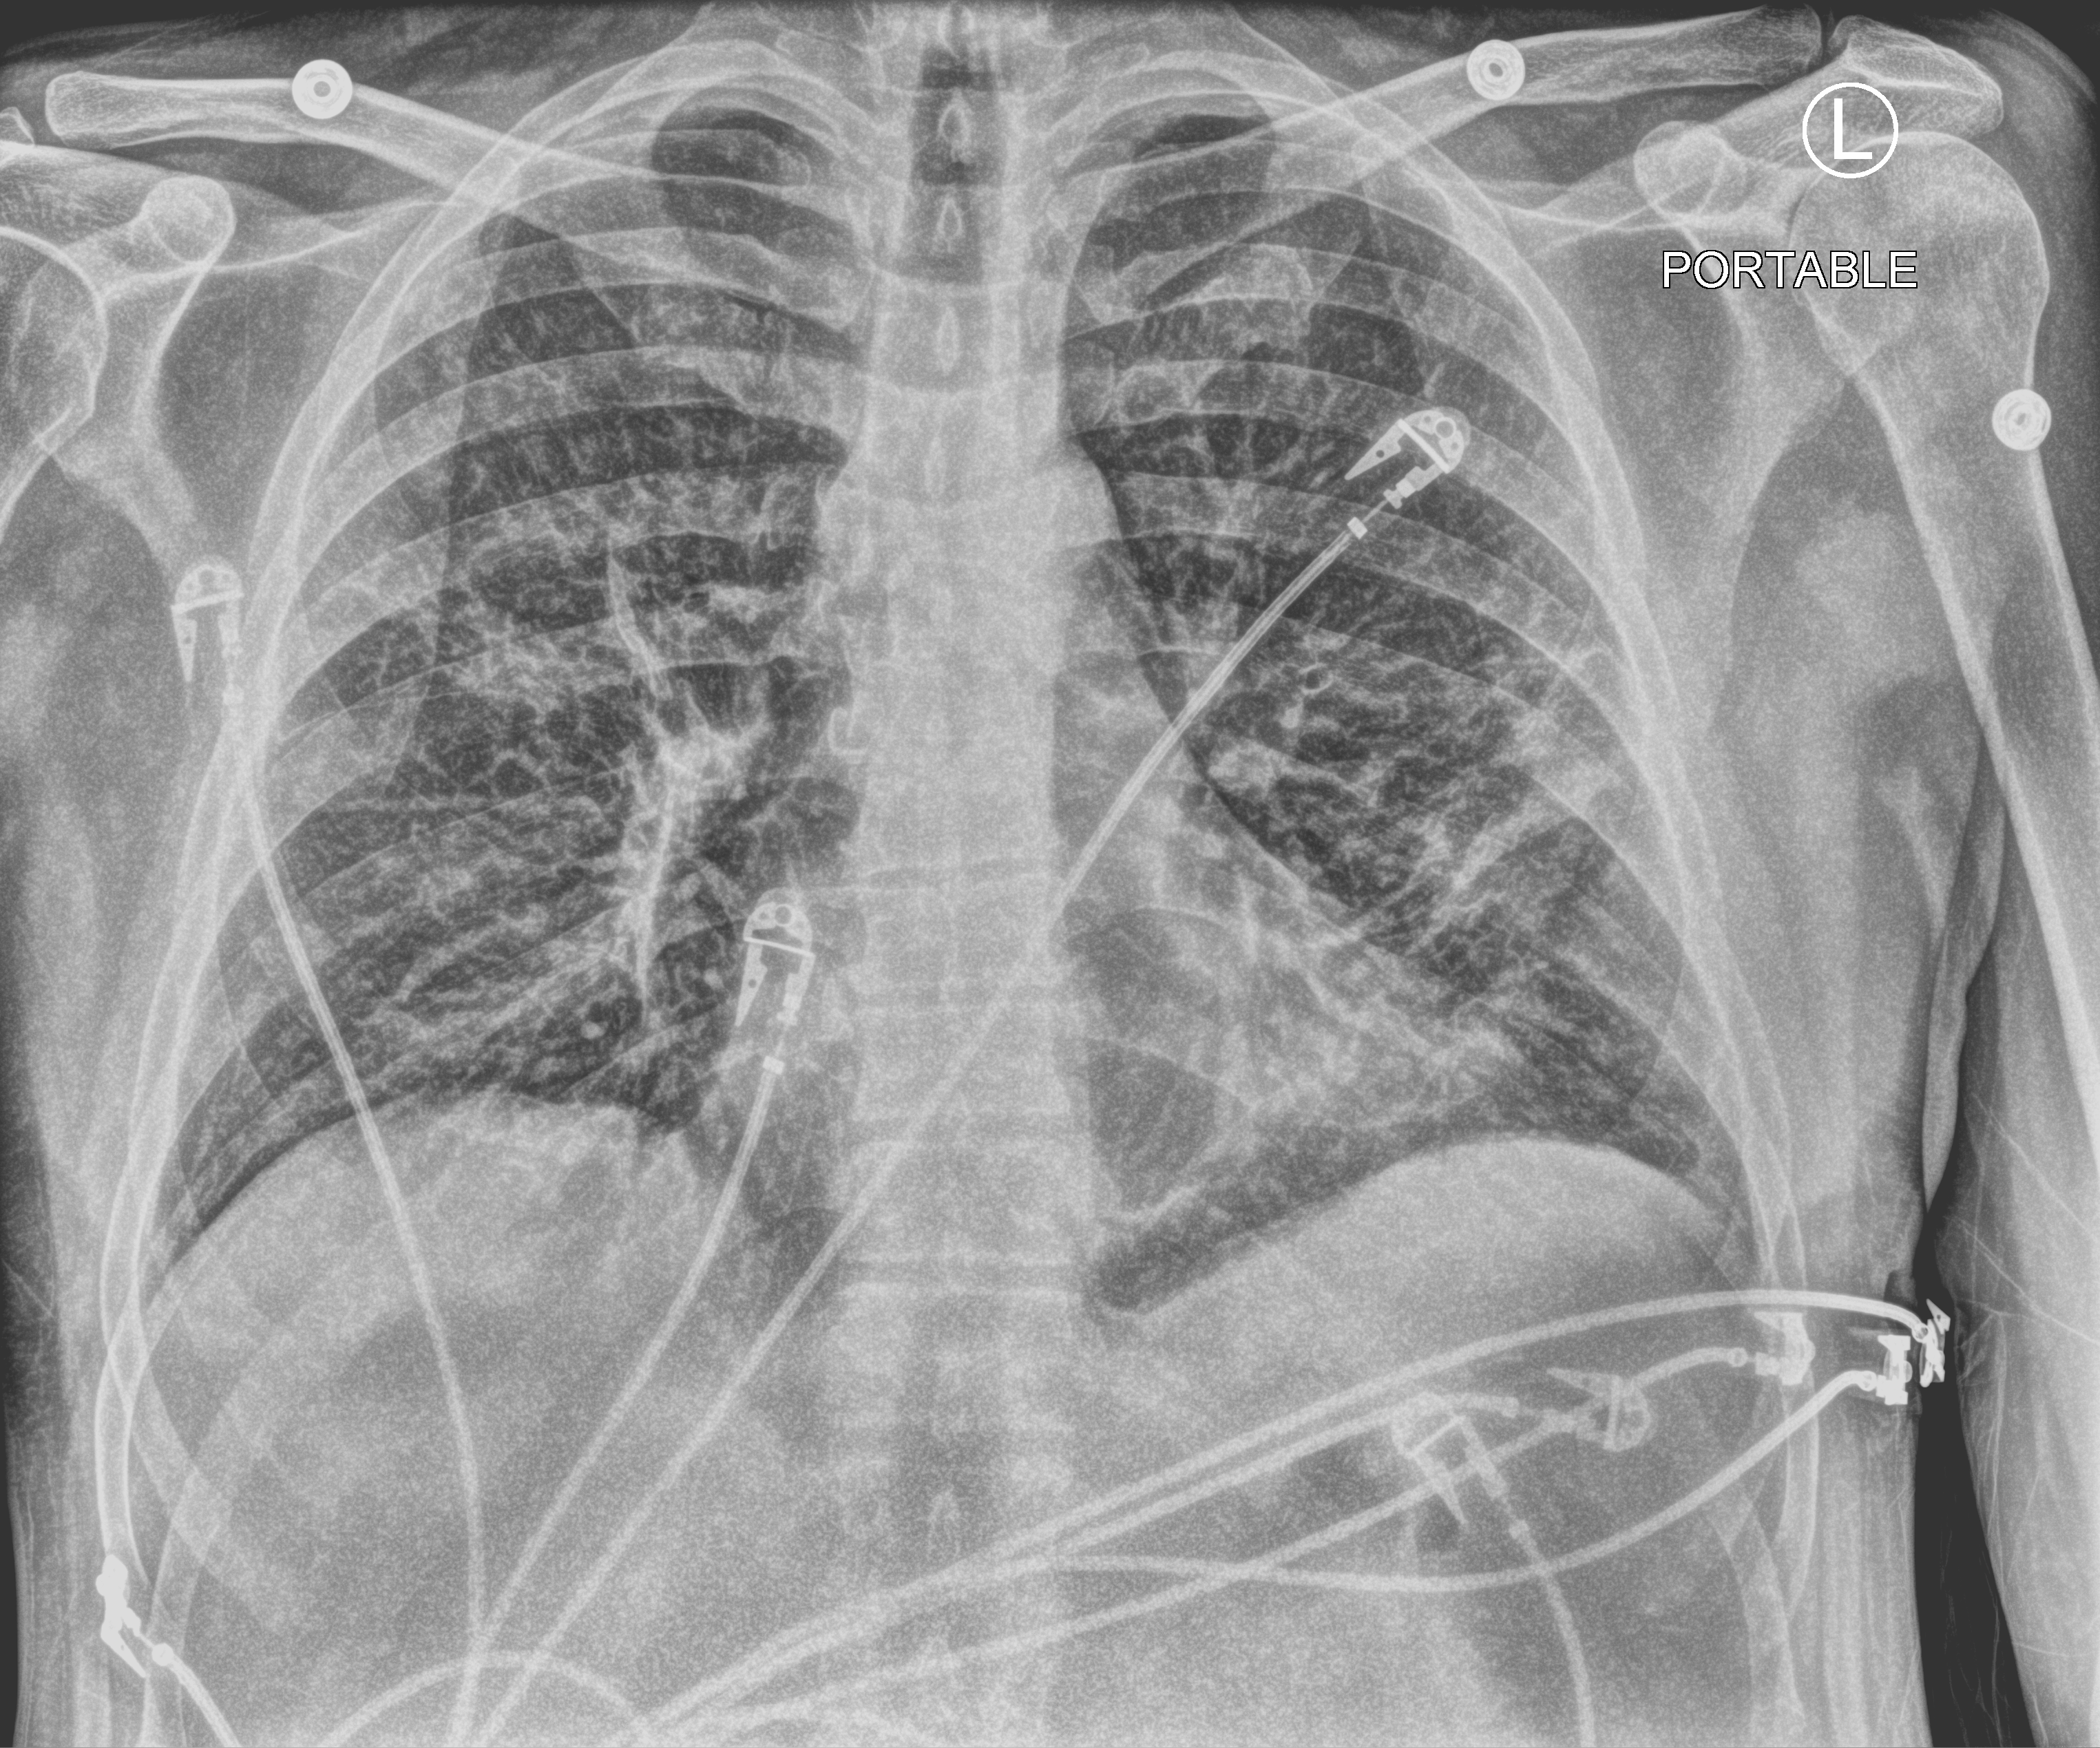
Bedside chest radiograph (computed radiography), anteroposterior (AP) projection. Patient hospitalised with COVID-19; male, aged 60–74 years.
From the hospital-stay record, not from the radiograph (when in the stay this image was taken is not recorded): admitted to intensive care during this hospital stay: no; COPD (admission record): no; mechanically ventilated during this hospital stay: no.